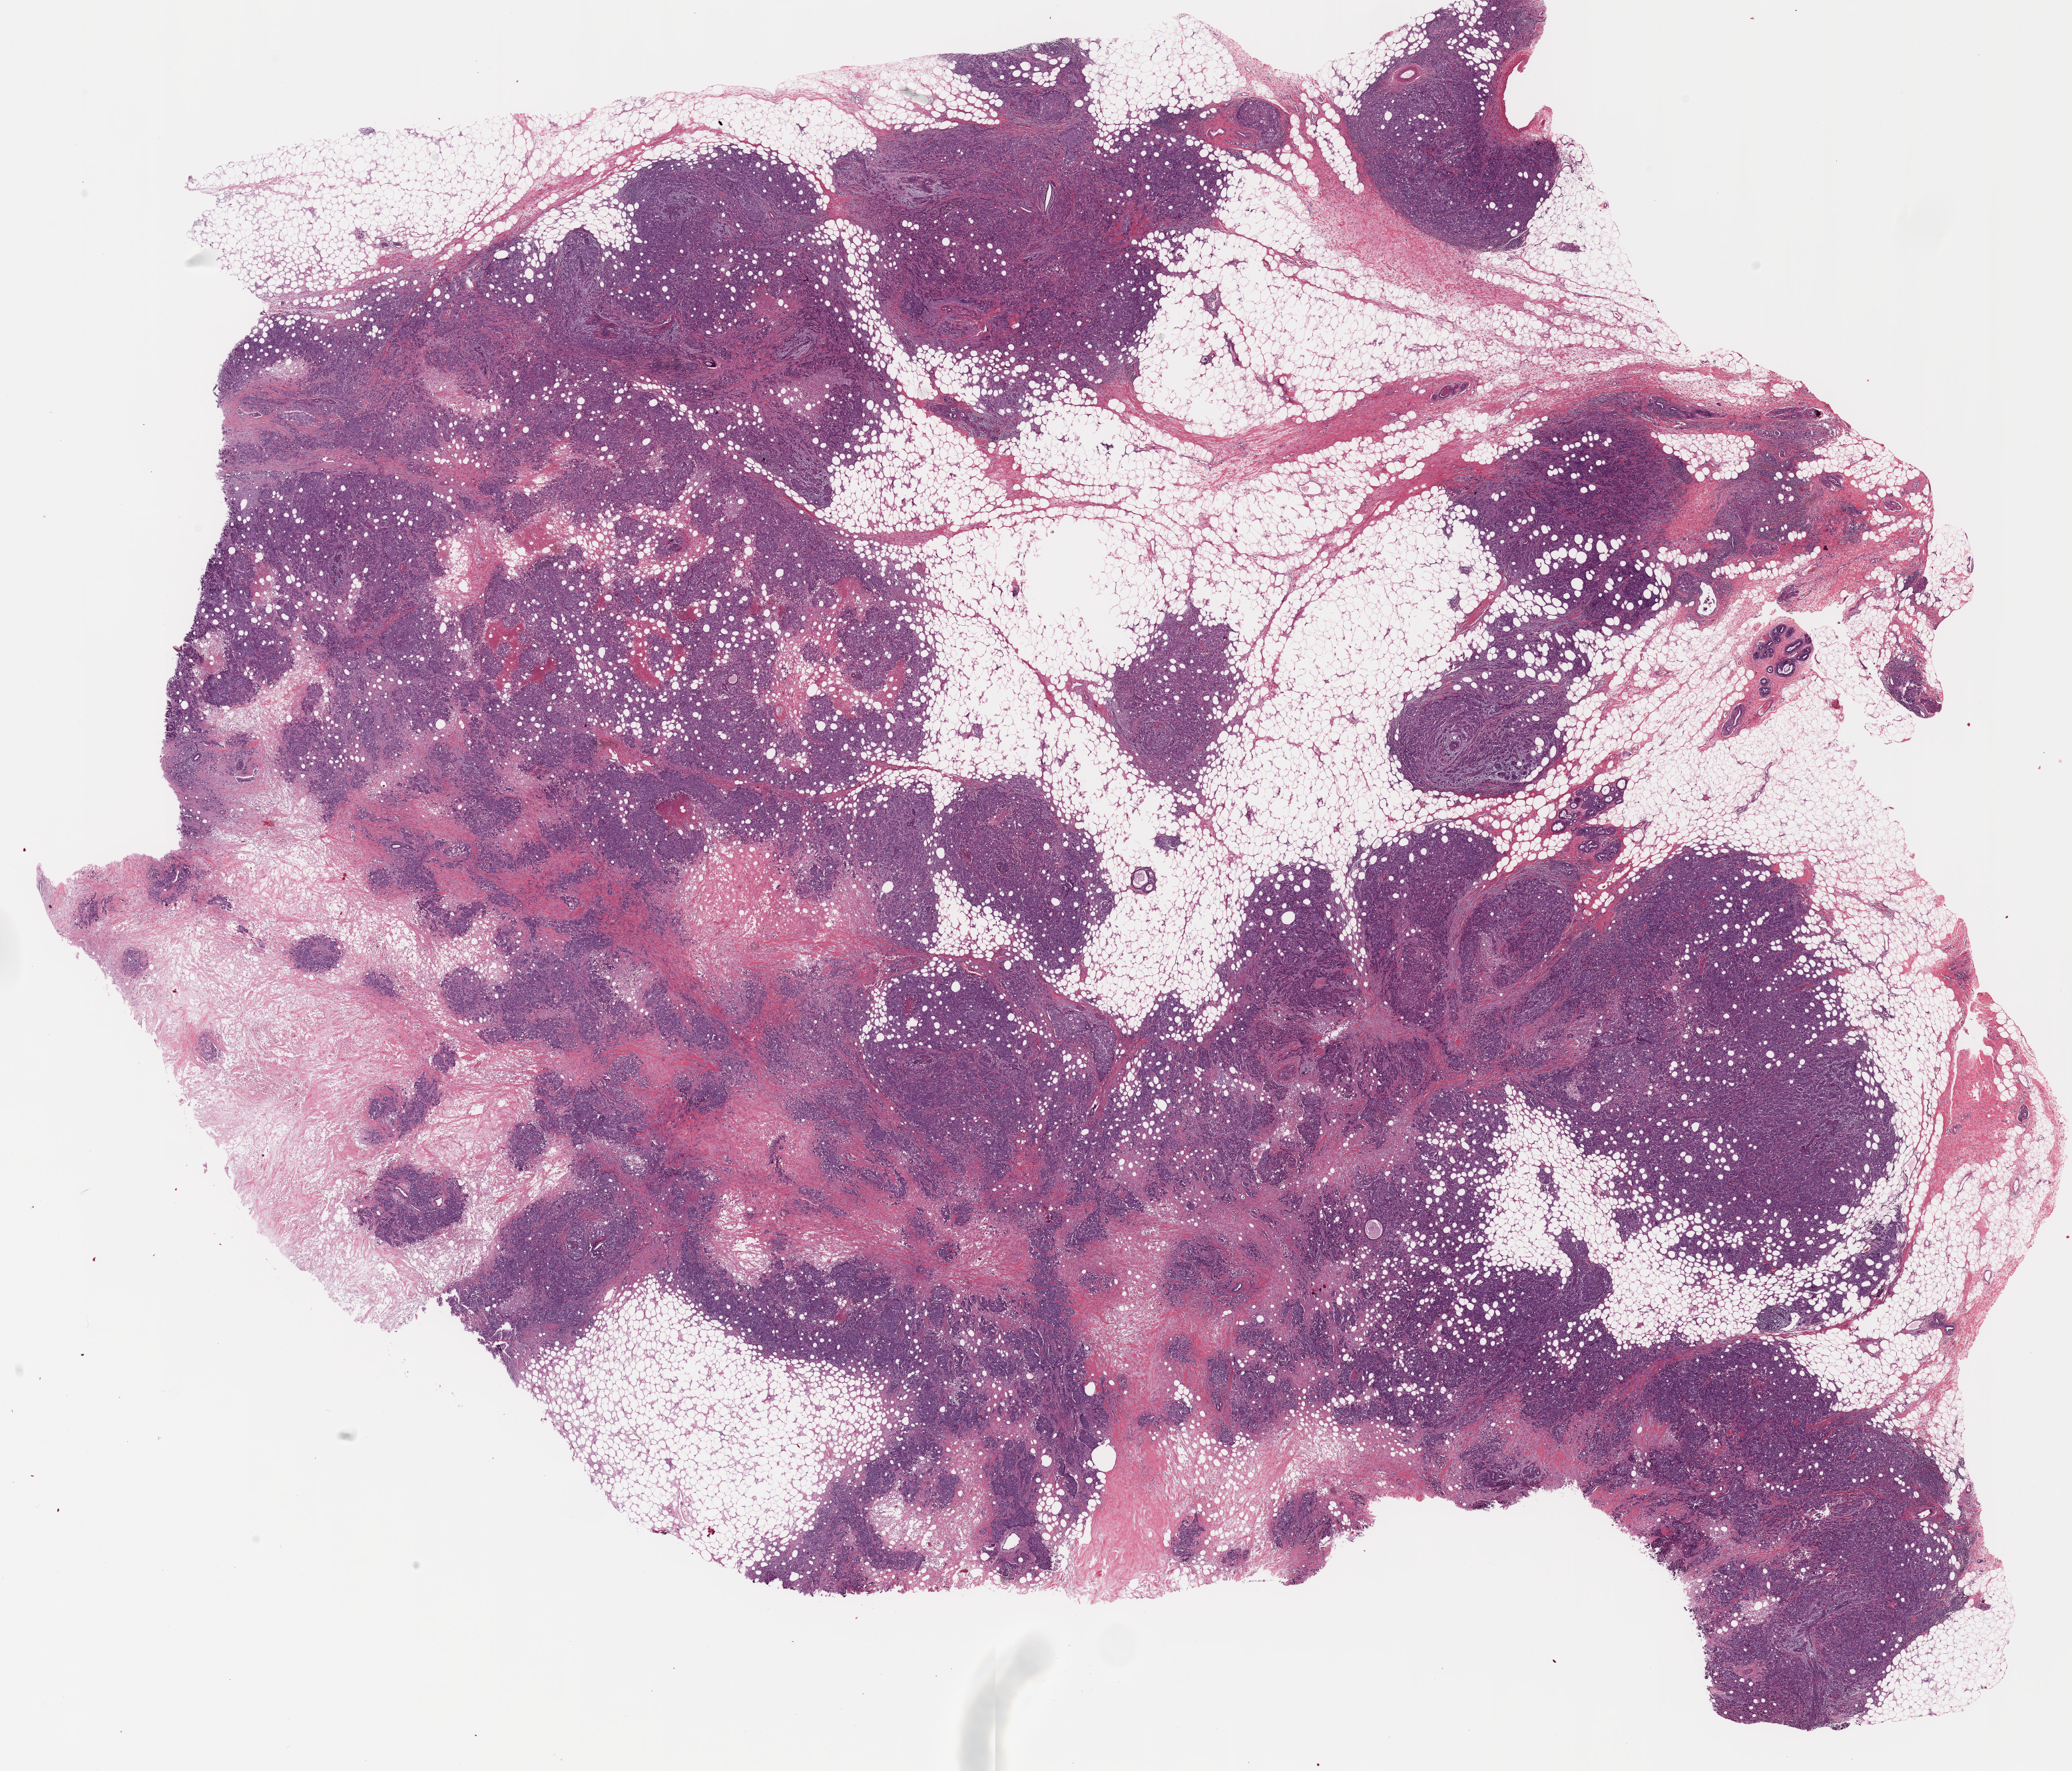
Hematoxylin and eosin (H&E) stained whole-slide image — whole scanned area (about 24.9 x 21.2 mm, from a 20x scan) shown as a low-resolution overview. Formalin-fixed paraffin-embedded (FFPE) diagnostic section. Sample: primary tumour, breast. Patient: female, age at initial diagnosis 59 years.
AJCC pathologic stage: IIIA. Lymph nodes positive (case pathology): 3 of 27 examined. Laterality: left. Histologic diagnosis: Infiltrating duct carcinoma, NOS.